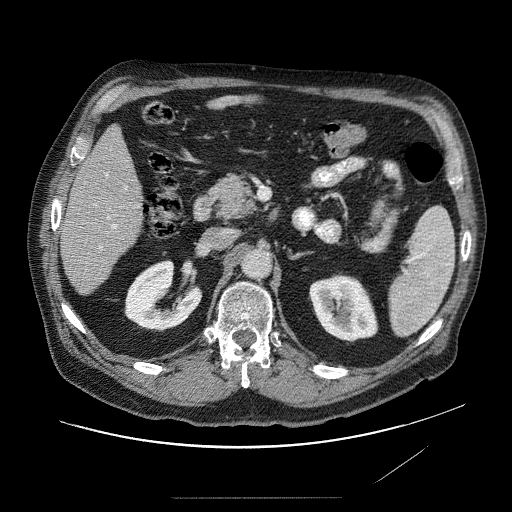
Contrast-enhanced abdominal CT (liver protocol), one axial slice. Position 27 of 89 along the scan axis. 120 kVp. Soft-tissue window (W 400 / L 40 HU). 2.5 mm slice thickness. 512 × 512 image matrix. From the clinical record (not read from this slice): diagnosis: hepatocellular carcinoma (patient treated with transarterial chemoembolisation; whether this scan precedes or follows treatment is not stated here); TNM stage (as recorded): Stage-IVA; Child-Pugh class: A.
Outlined on this slice (semi-automatic segmentation, software-assisted and operator-edited):
- liver parenchyma outside the tumour (the mass and vessels are separate outlines, so this box may not span the whole liver): box from (x=60, y=126) to (x=150, y=296) px
- liver vessels: (x=100, y=141)–(x=134, y=255)